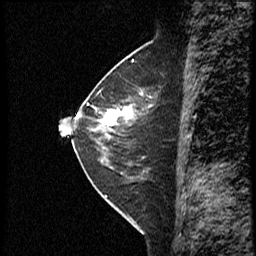
Breast MRI (dynamic contrast-enhanced), one sagittal slice. Position 18 of 40 along the scan axis. Dynamic contrast-enhanced study with each time point stored as its own series, time point 2 of 4 at this slice position (early post-contrast, ordered by acquisition time). 1.5 T. TE 4.2 ms, TR 18.8 ms. 3 mm slice thickness. 256 × 256 image matrix, field of view 200 × 200 mm. Female patient. From the clinical record (not read from this slice): setting: breast cancer imaged before/during neoadjuvant chemotherapy; receptor status: HER2-positive.
Structures marked on this image (semi-automatically segmented with operator editing):
- analysis volume of interest (the breast-tissue region the enhancement analysis was run in; not a lesion): bounding box [x1, y1, x2, y2] px = [91, 79, 162, 153]
- tumour enhancement mask (voxels above the 100 % enhancement threshold inside the analysis volume of interest): [101, 105, 136, 126]